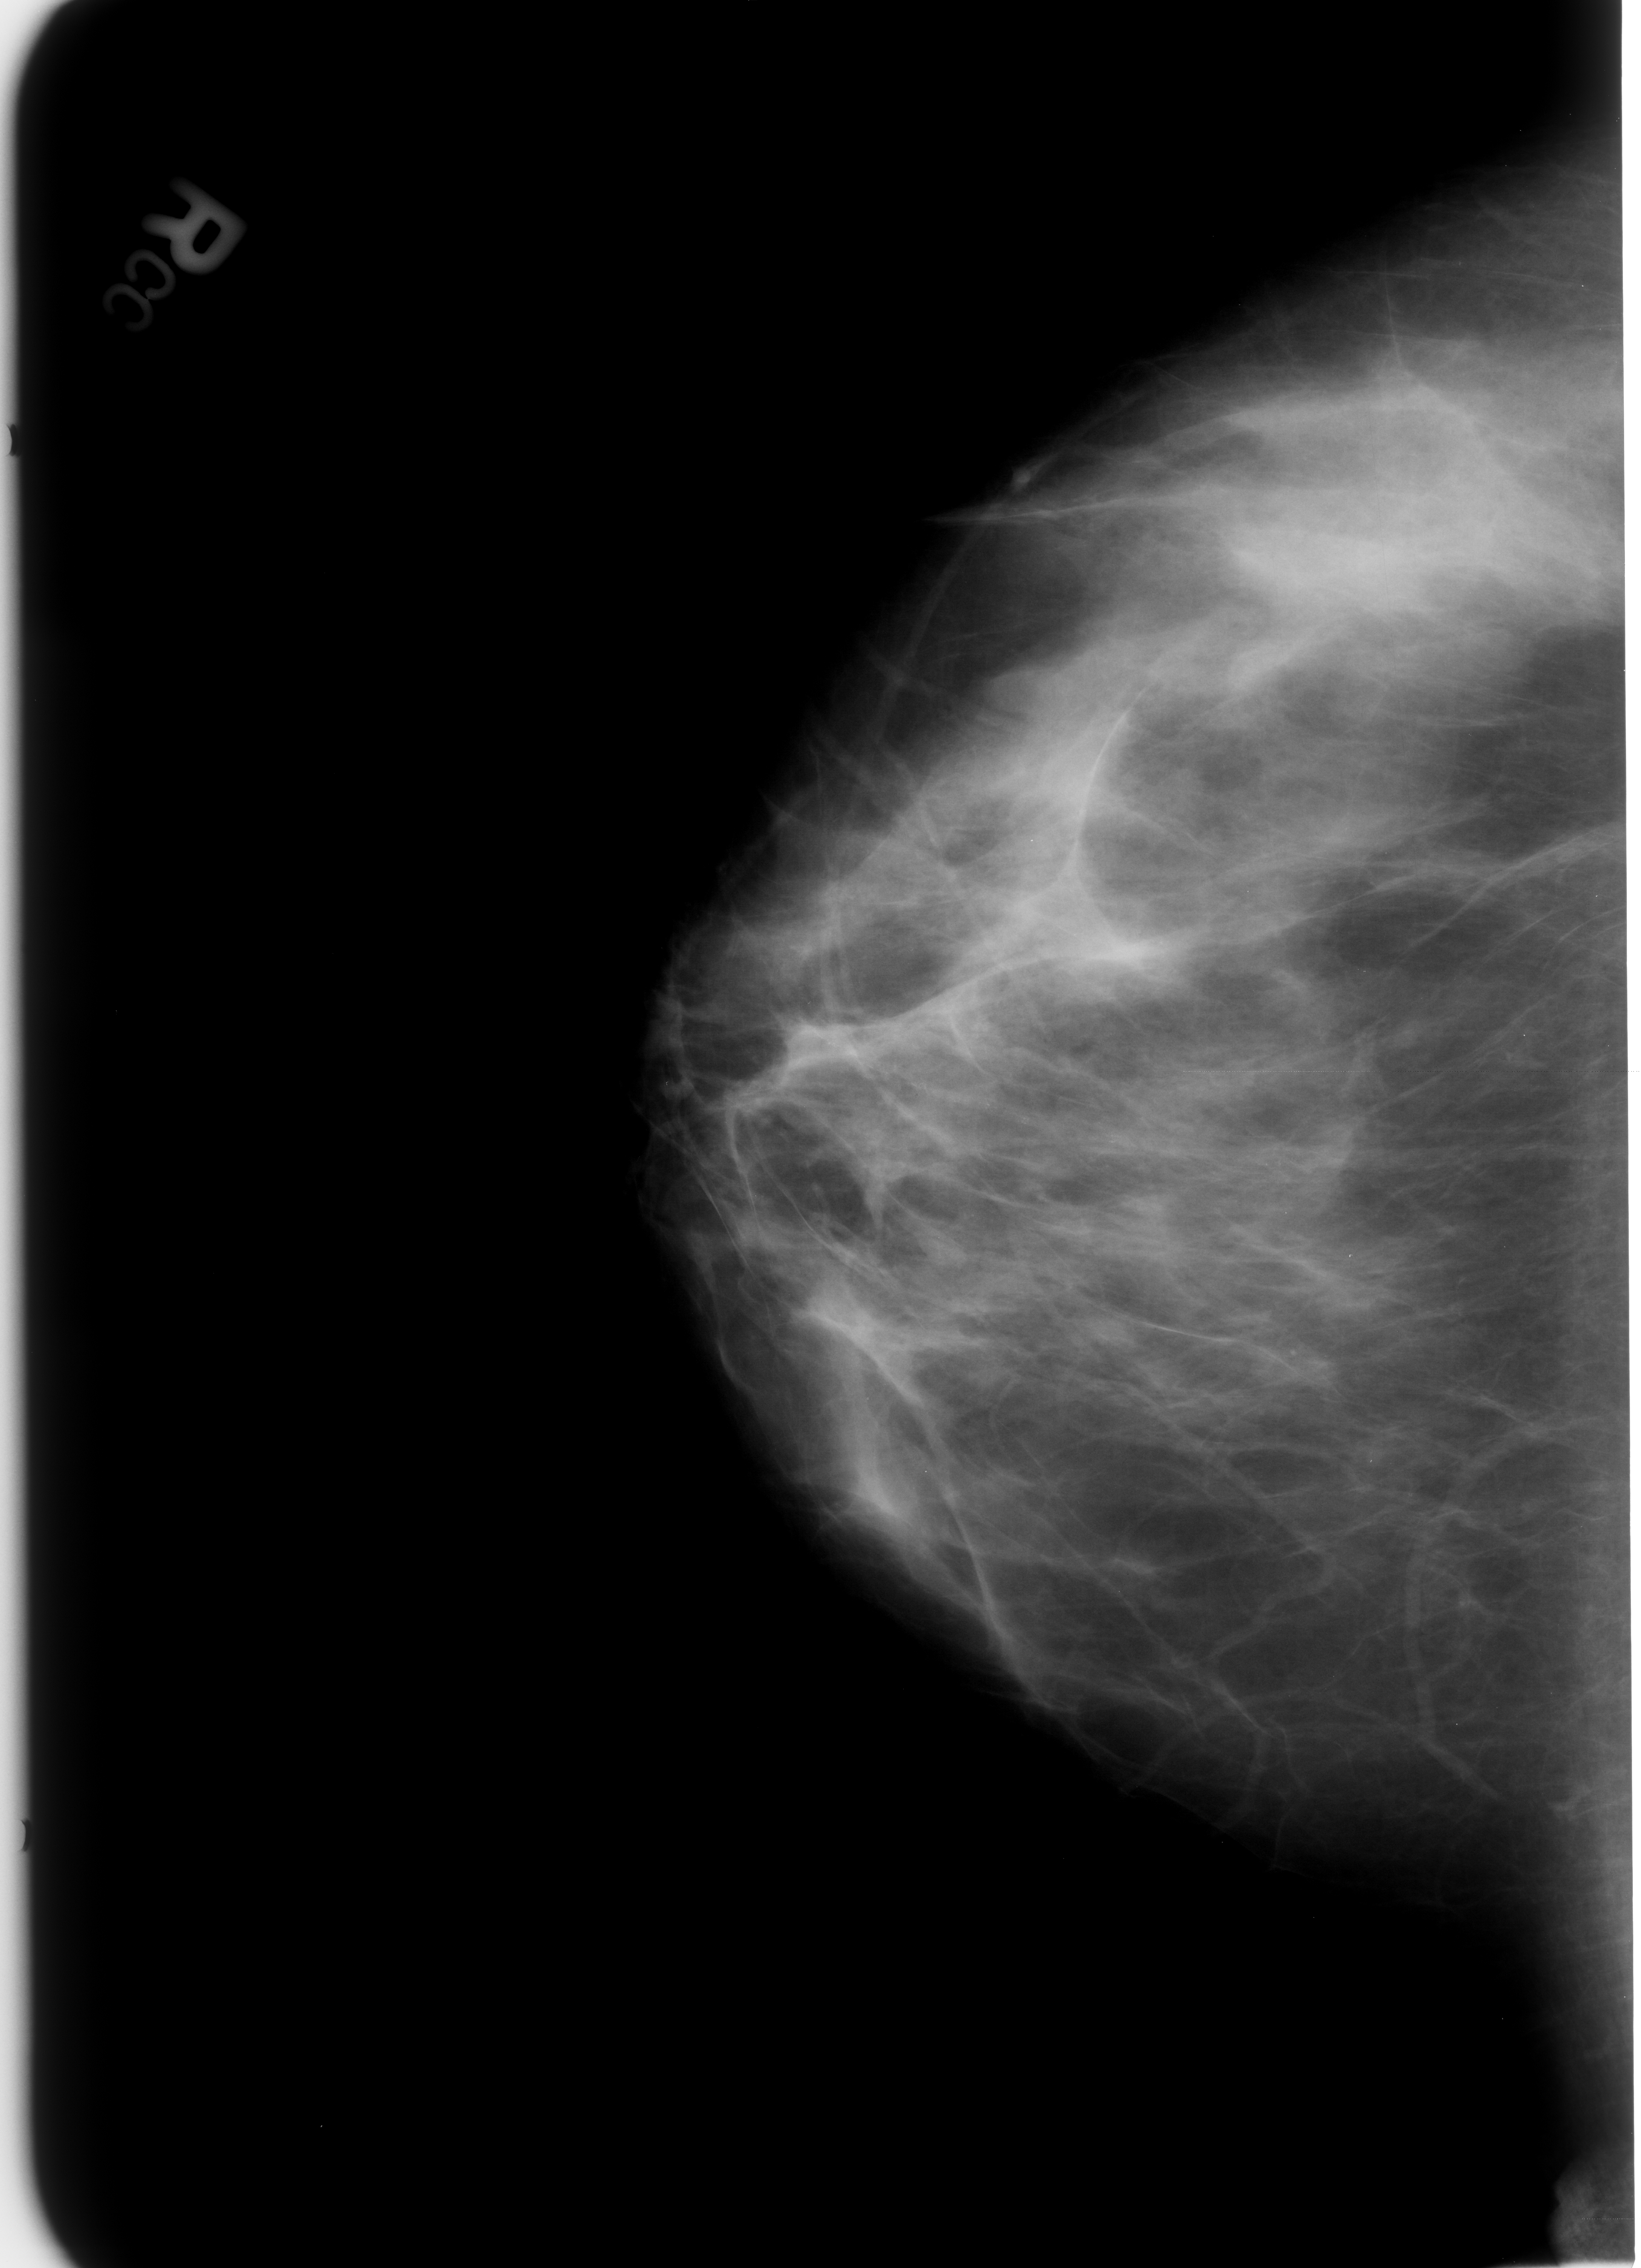
Digitized screen-film mammogram, right breast, CC view, breast composition: heterogeneously dense (BI-RADS density category 3 of 4).
Marked abnormality: calcifications, morphology vascular; BI-RADS assessment category 2; subtlety rating 3 on a 1 (subtle) to 5 (obvious) scale; benign without callback (not worked up further).